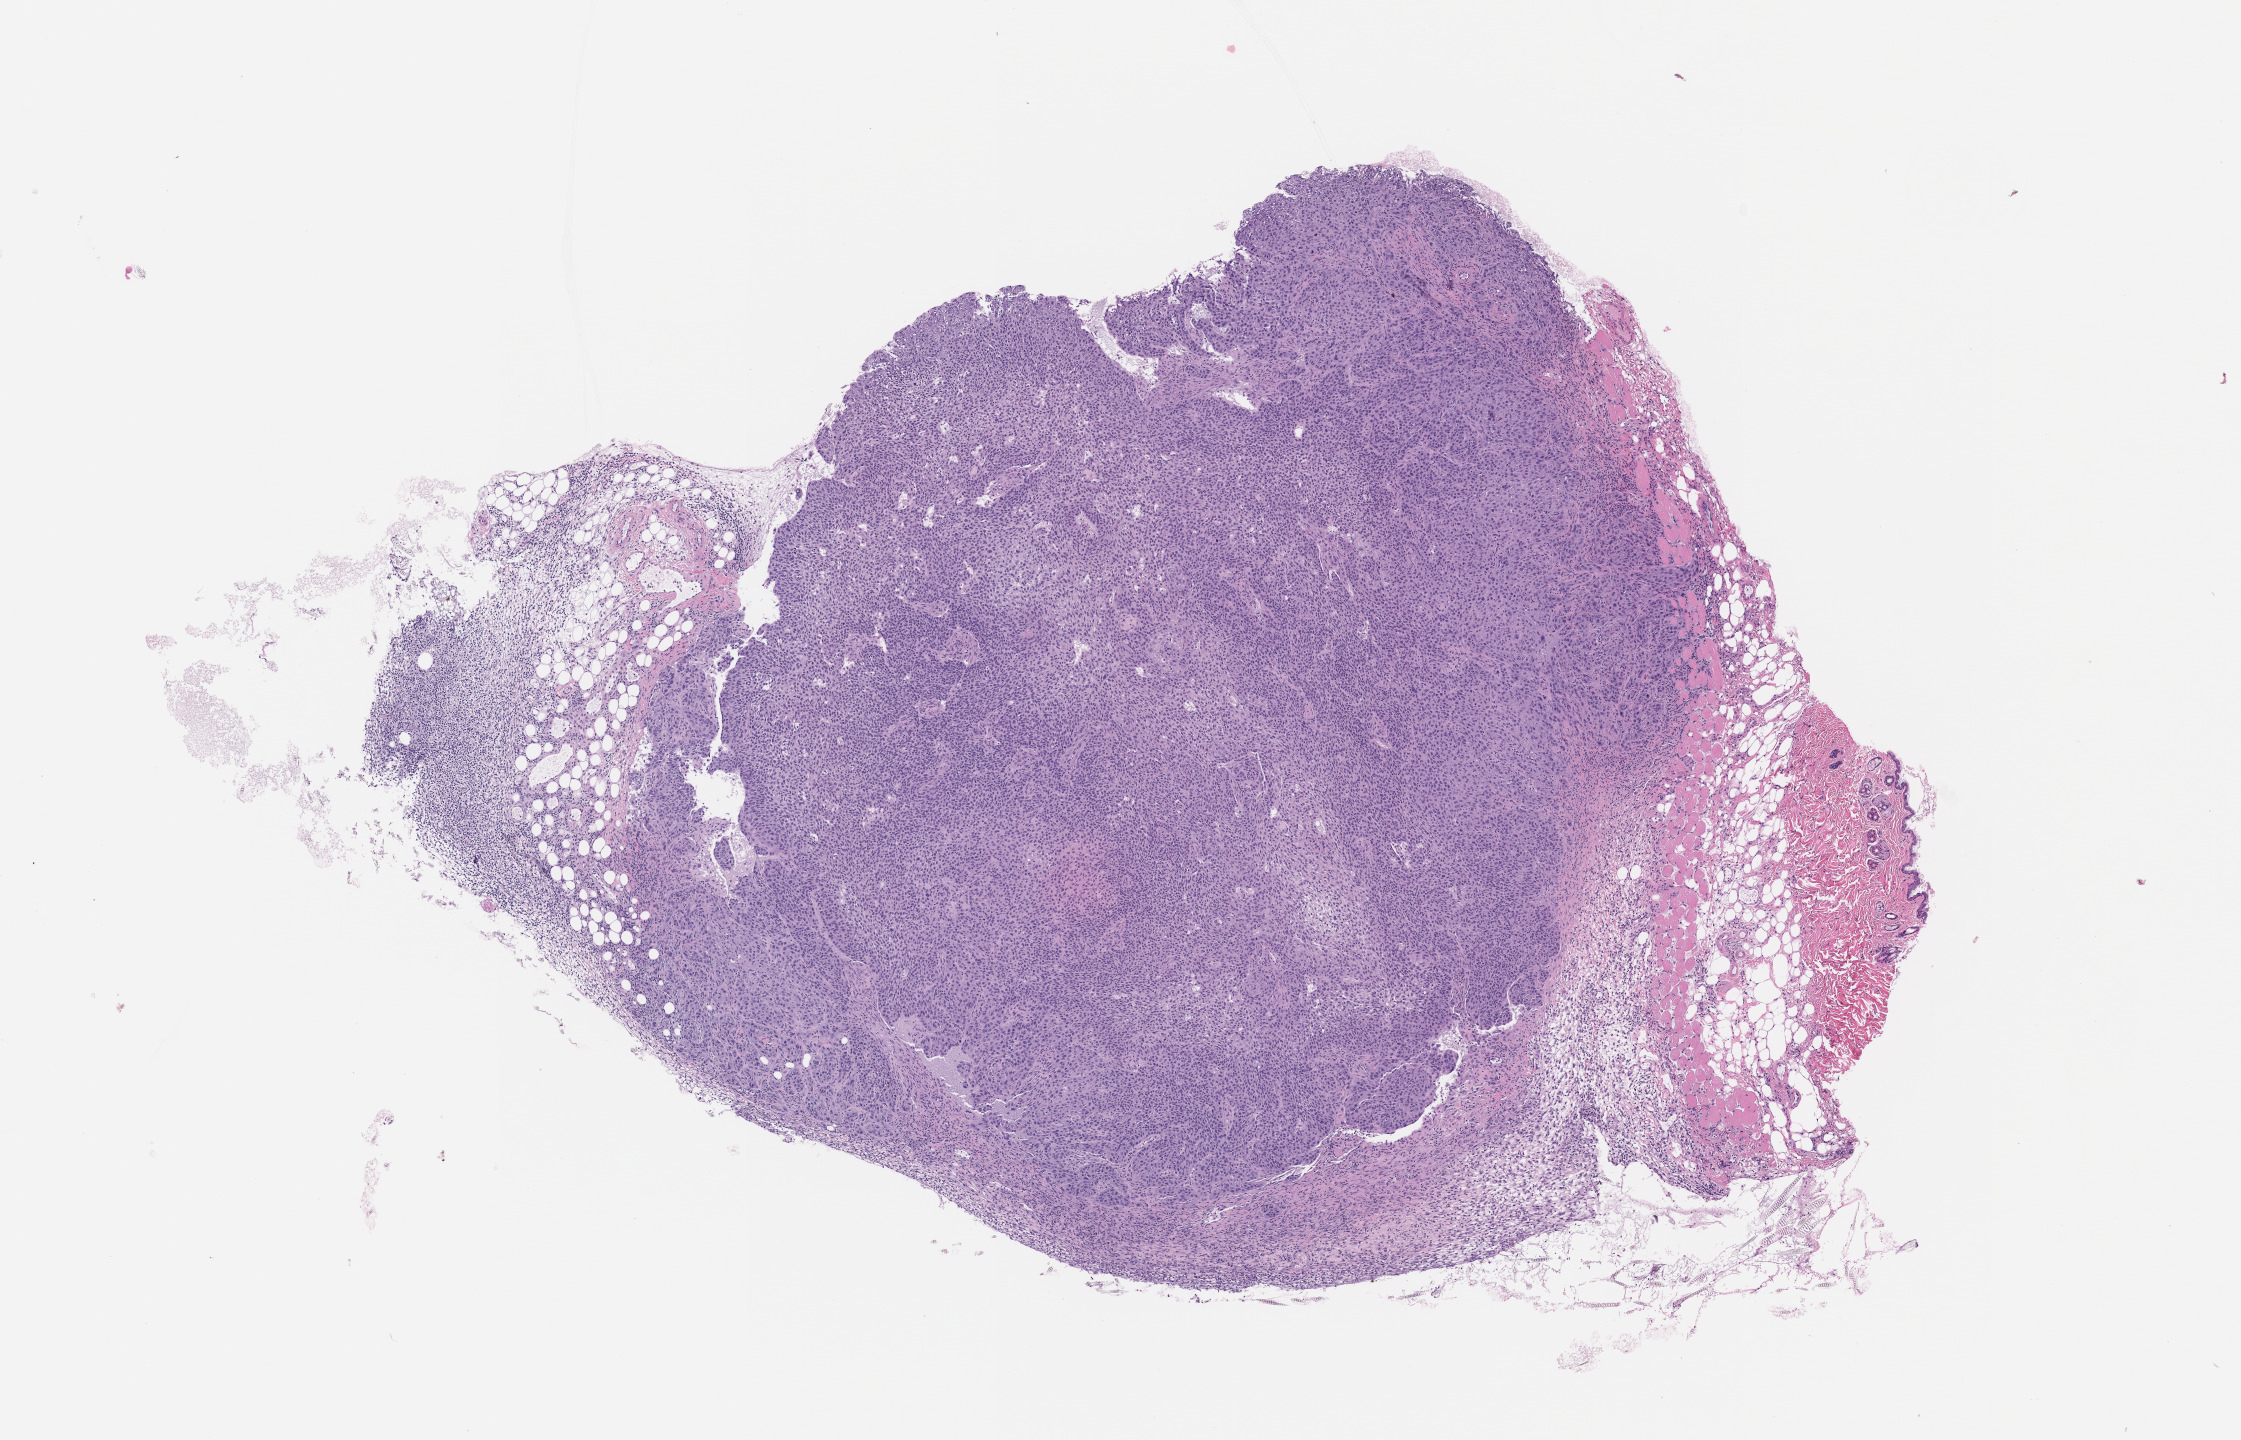
Haematoxylin and eosin whole-slide image of a patient-derived xenograft (PDX) tumor grown in a mouse, passage 2, whole scanned area (about 9.0 x 5.8 mm) shown as a low-resolution overview. Formalin-fixed, paraffin-embedded (FFPE) tissue. Originating tumor site category: bladder.
Originating patient diagnosis: Transitional Cell Carcinoma.